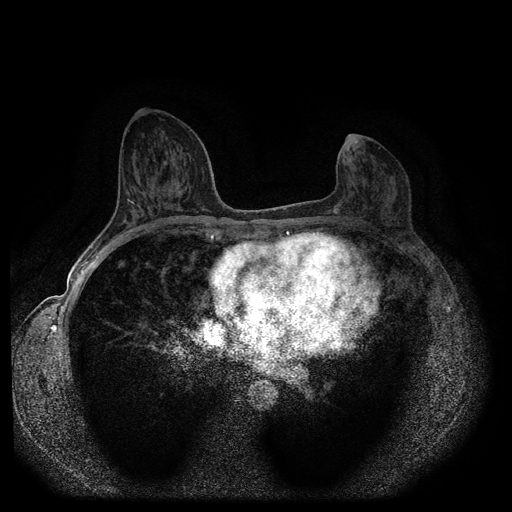
Breast MRI (dynamic contrast-enhanced, multi-phase), one axial slice; slice 49 of 116 in the series (ordered by position); dynamic contrast-enhanced series, time point 2 of 5 at this slice position (early post-contrast); 1.5 T; TE 2.6 ms, TR 5.4 ms; 2 mm slice thickness; 512 × 512 image matrix, field of view 340 × 340 mm. Female patient, age 57 years.
Outlined on this slice (semi-automatic segmentation, software-assisted and operator-edited):
- breast lesion (labelled 'tumour' in the annotation; benign lesions carry a separate 'benign' label): bounding box <333,200,343,215> (left, top, right, bottom; pixels)